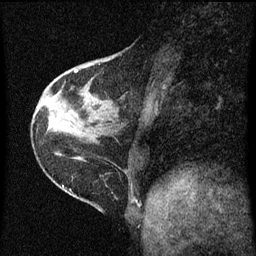
Breast MRI (dynamic contrast-enhanced), one sagittal slice. Slice 25 of 60 in the series (ordered by position). Dynamic contrast-enhanced series, image 2 of 3 at this slice position (ordered by acquisition). 1.5 T. TE 4.2 ms, TR 8 ms. 256 × 256 image matrix. Patient: female, 38 years.
Annotated regions visible in this slice (semi-automatic segmentation, software-assisted and operator-edited):
- analysis volume of interest (the breast-tissue region the enhancement analysis was run in; not a lesion): box from (x=67, y=48) to (x=128, y=131) px
- tumour enhancement mask (voxels above the 70 % enhancement threshold inside the analysis volume of interest): (x=74, y=64)–(x=93, y=73)